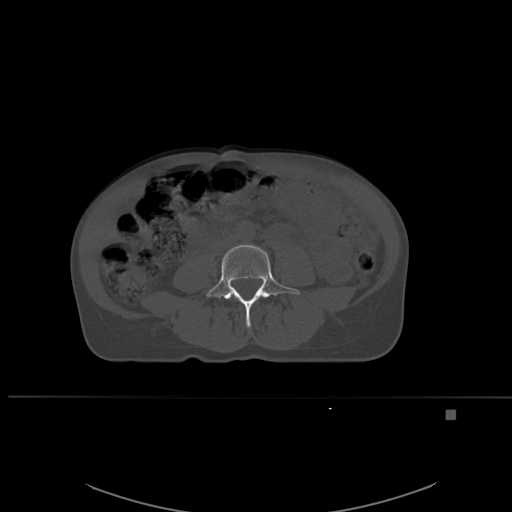
CT including the spine, one axial slice. Position 194 of 537 along the scan axis. Bone window (W 1800 / L 400 HU). 512 × 512 image matrix, field of view 440 × 440 mm. Patient: female, 45 years. Case-level facts recorded for this patient, not image findings: primary cancer: lung.
Annotated regions visible in this slice (semi-automatically segmented with operator editing):
- L4 vertebra: bounding box [x1, y1, x2, y2] px = [205, 243, 301, 328]